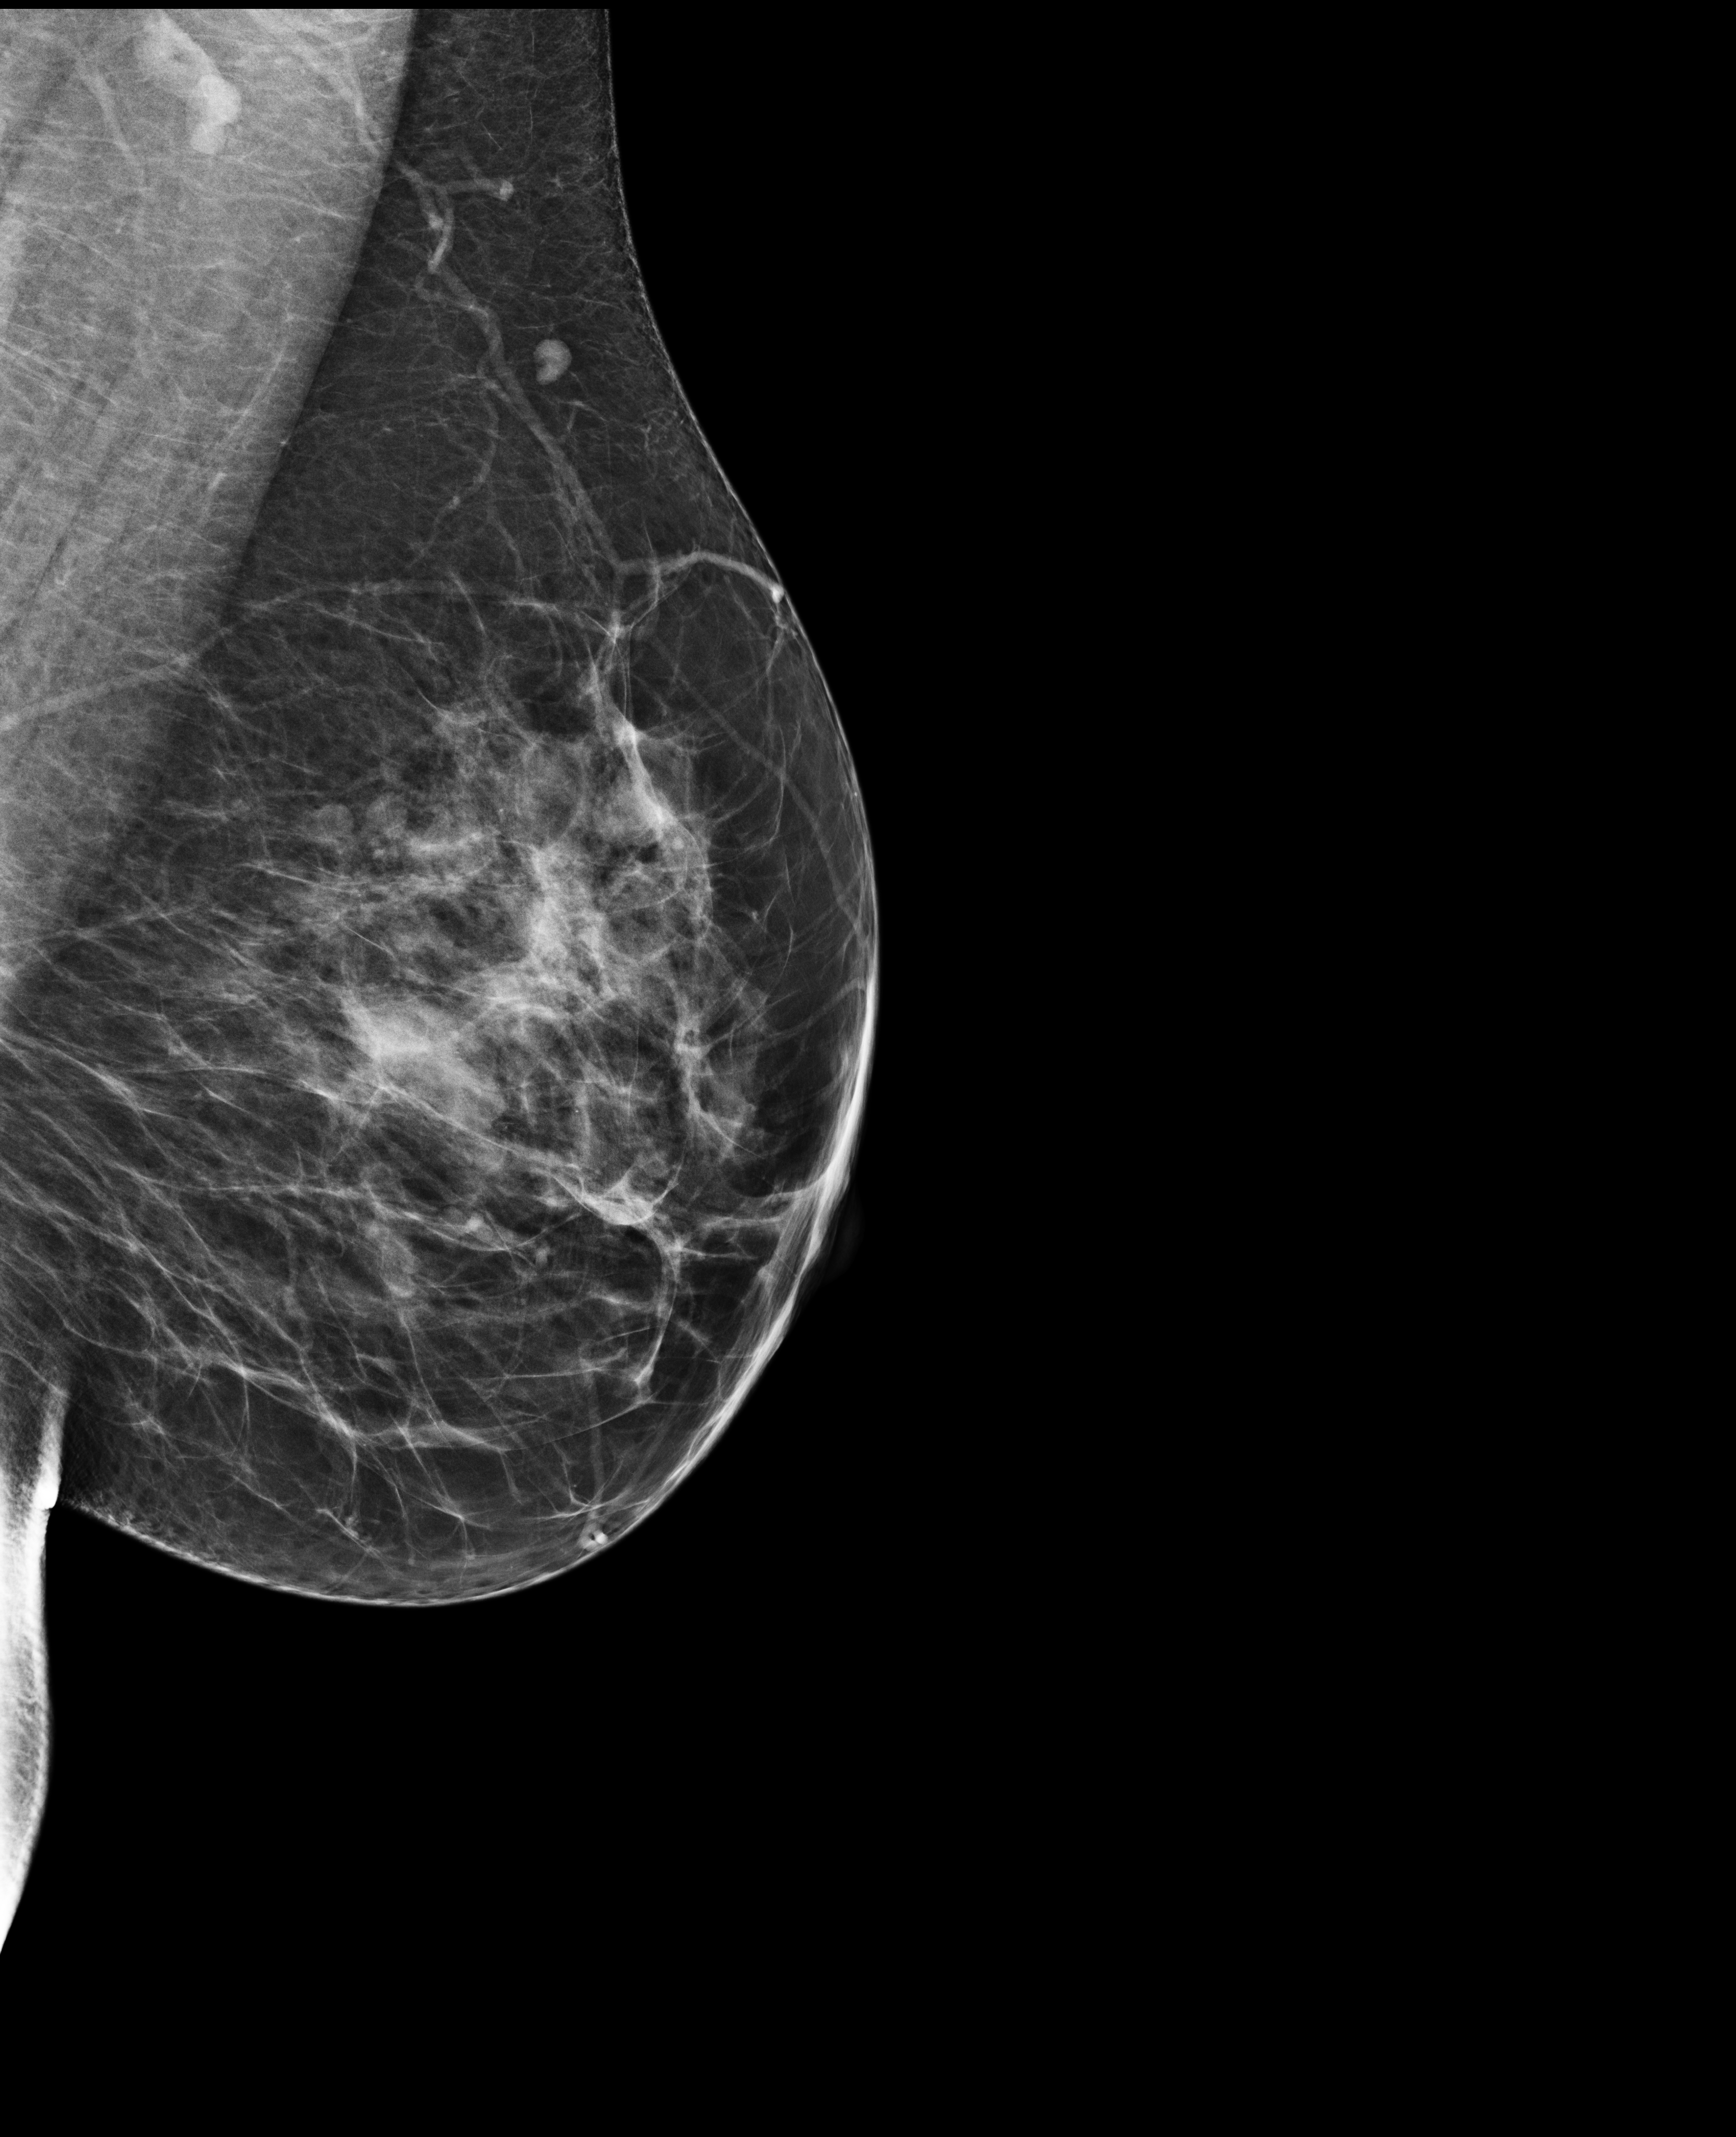
Full-field digital mammogram (FFDM), left breast, MLO view, screening examination, system: Selenia Dimensions. Female patient, age 44 years.
Final BI-RADS assessment for this screening round (tomosynthesis exam, both breasts): category 2.